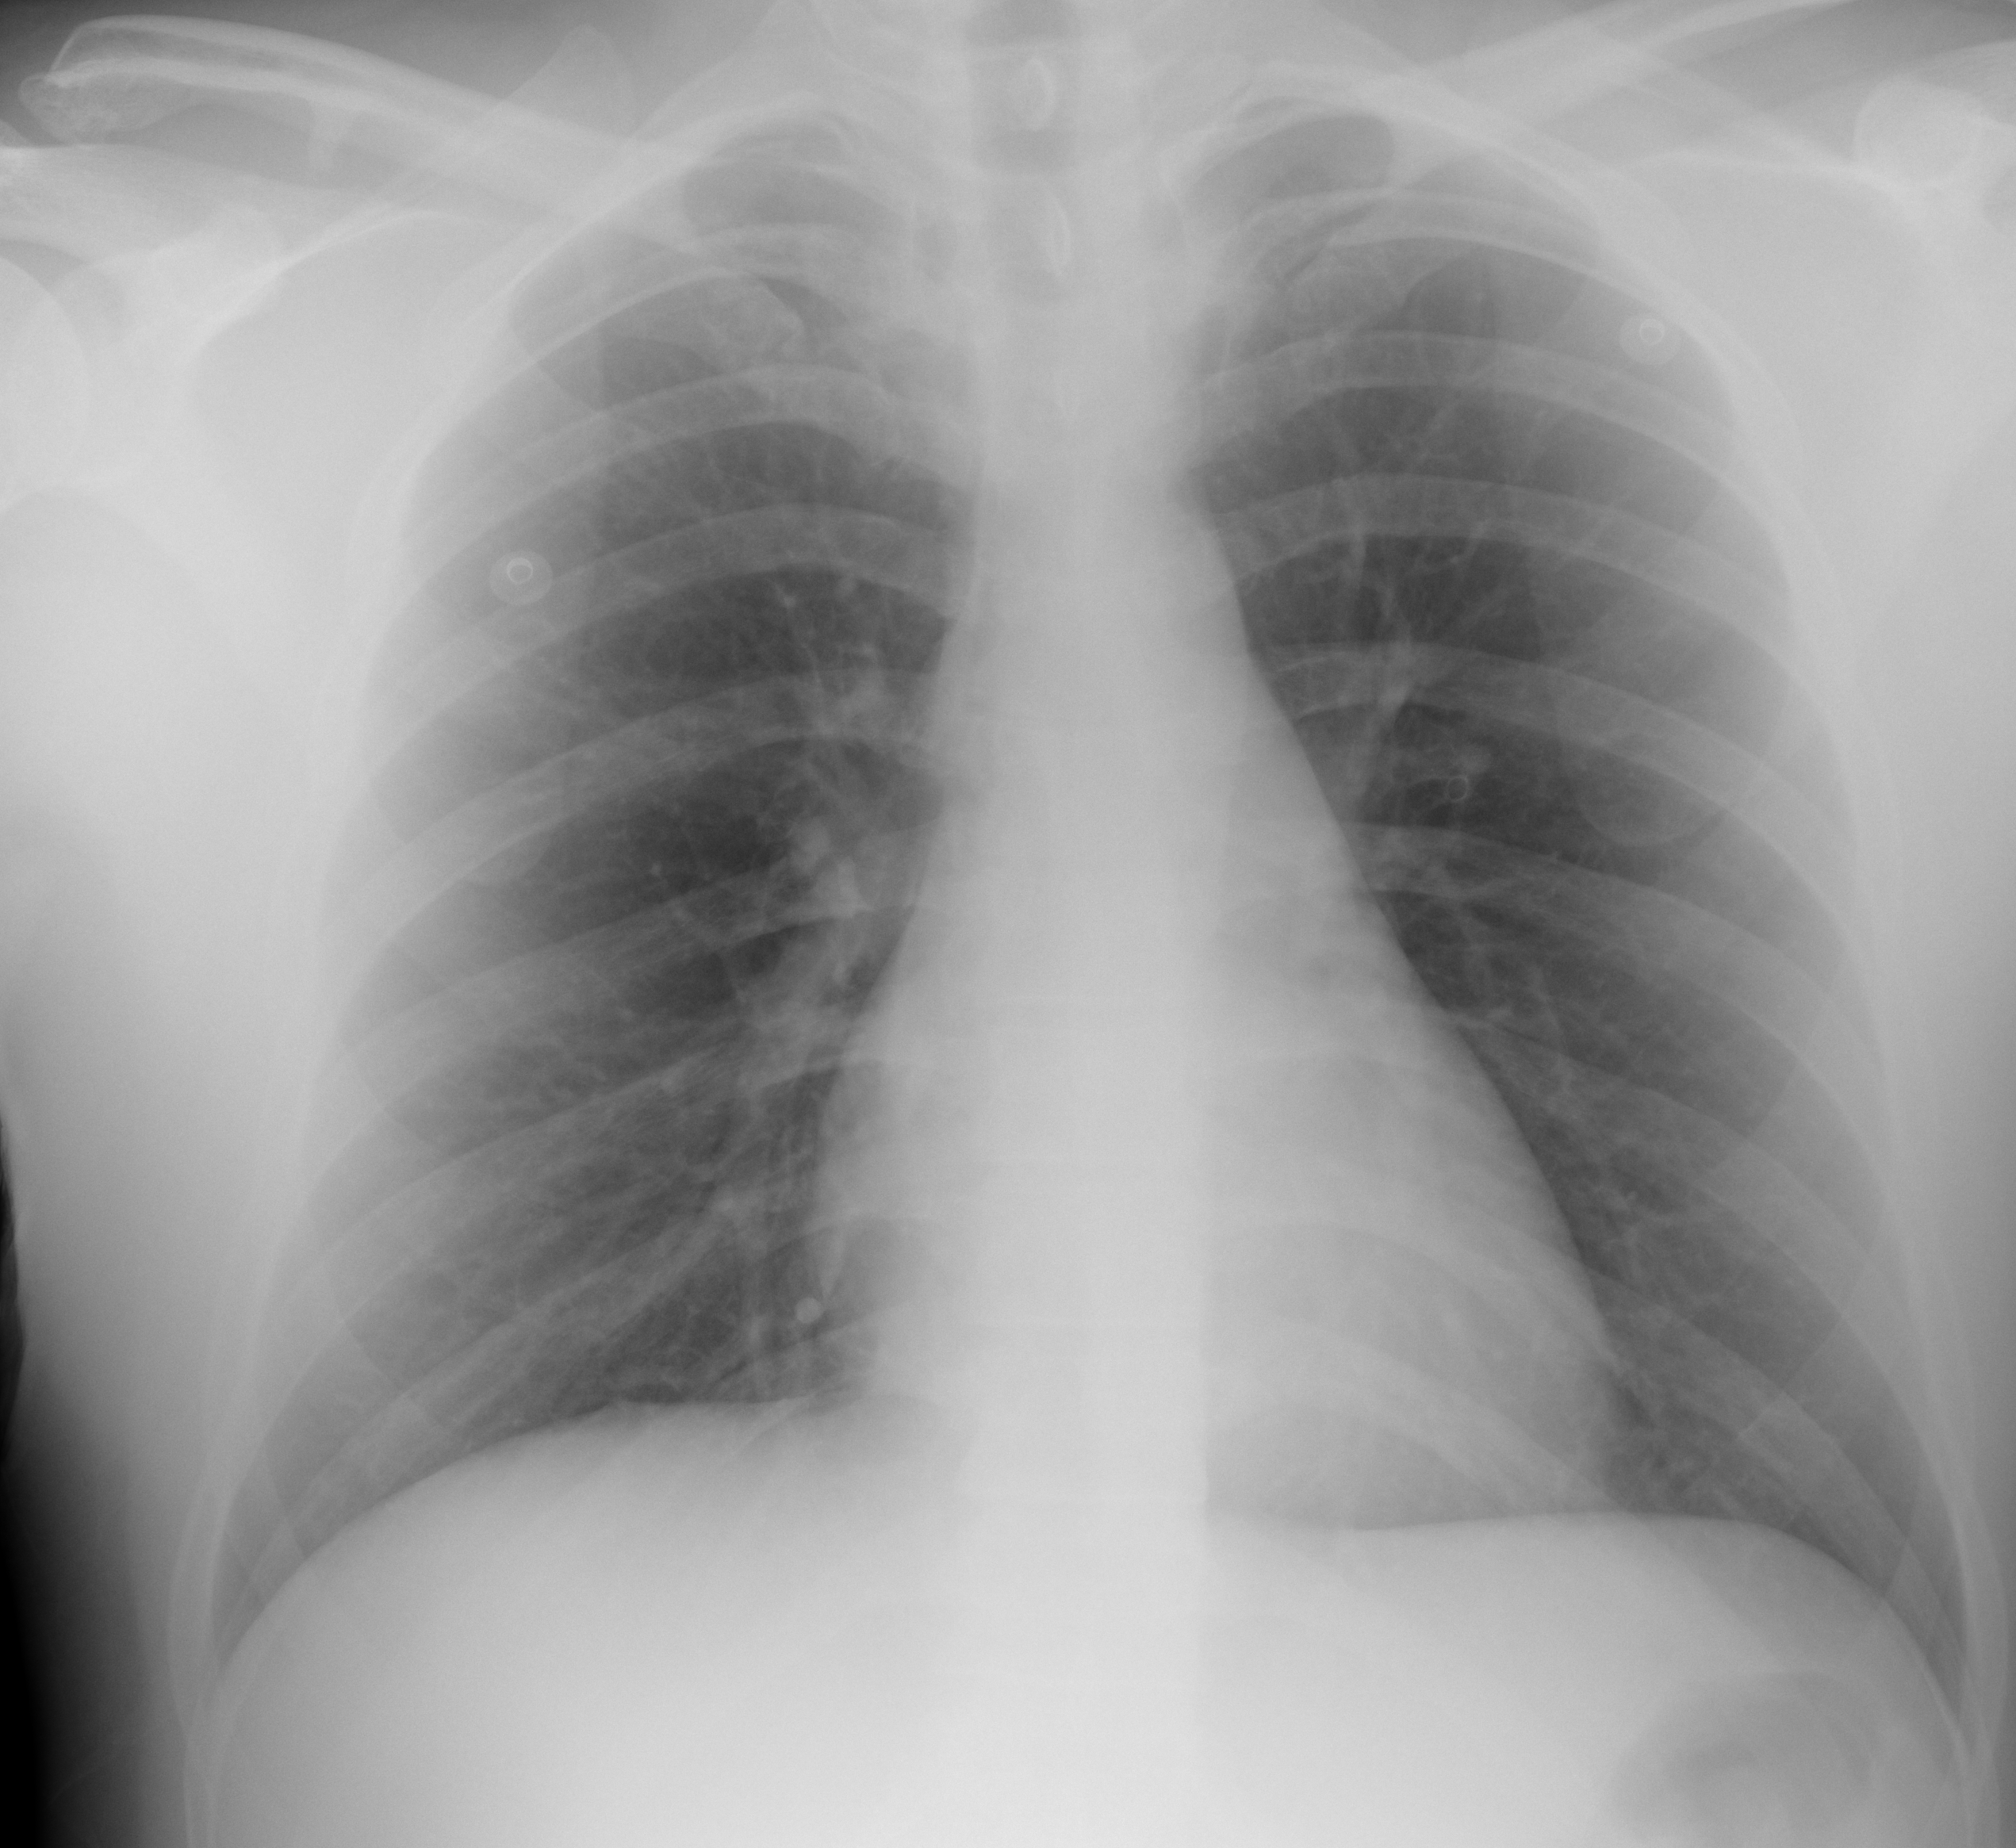
Portable chest radiograph, AP projection. Male patient, age 30 years; imaged 7 days after the COVID-19 diagnosis.
Key findings recorded by the radiologist: Both lungs are clear.